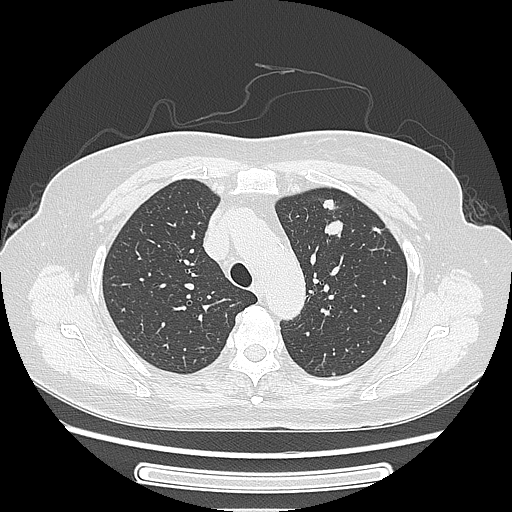
Chest CT, one axial slice; position 178 of 227 along the scan axis; reconstruction kernel LUNG; lung window (W 1500 / L -600 HU); 1.25 mm slice thickness; 512 × 512 image matrix. Female patient, age 77 years. Case-level facts recorded for this patient, not image findings: clinical TNM (as recorded): T1c N3 M0; histopathological grade: G2-3.
Structures marked on this image (bounding box drawn by a radiologist):
- lung tumour (recorded histology: adenocarcinoma): box from (x=321, y=189) to (x=350, y=243) px